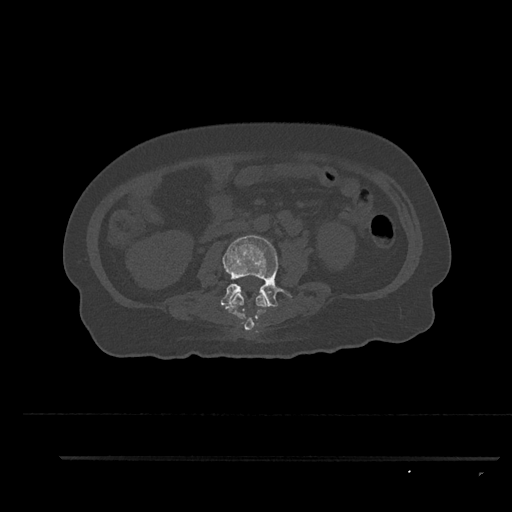
CT including the spine, one axial slice. Slice 110 of 797 in the series (ordered by position). Reconstruction kernel Br40s/3. 120 kVp. Bone window (W 1800 / L 400 HU). 0.5 mm slice thickness. 512 × 512 image matrix. Female patient, age 44 years. From the clinical record (not read from this slice): primary cancer: renal.
Outlined on this slice (semi-automatic segmentation, software-assisted and operator-edited):
- L2 vertebra: box from (x=226, y=293) to (x=267, y=332) px
- L3 vertebra: (x=220, y=235)–(x=292, y=309)